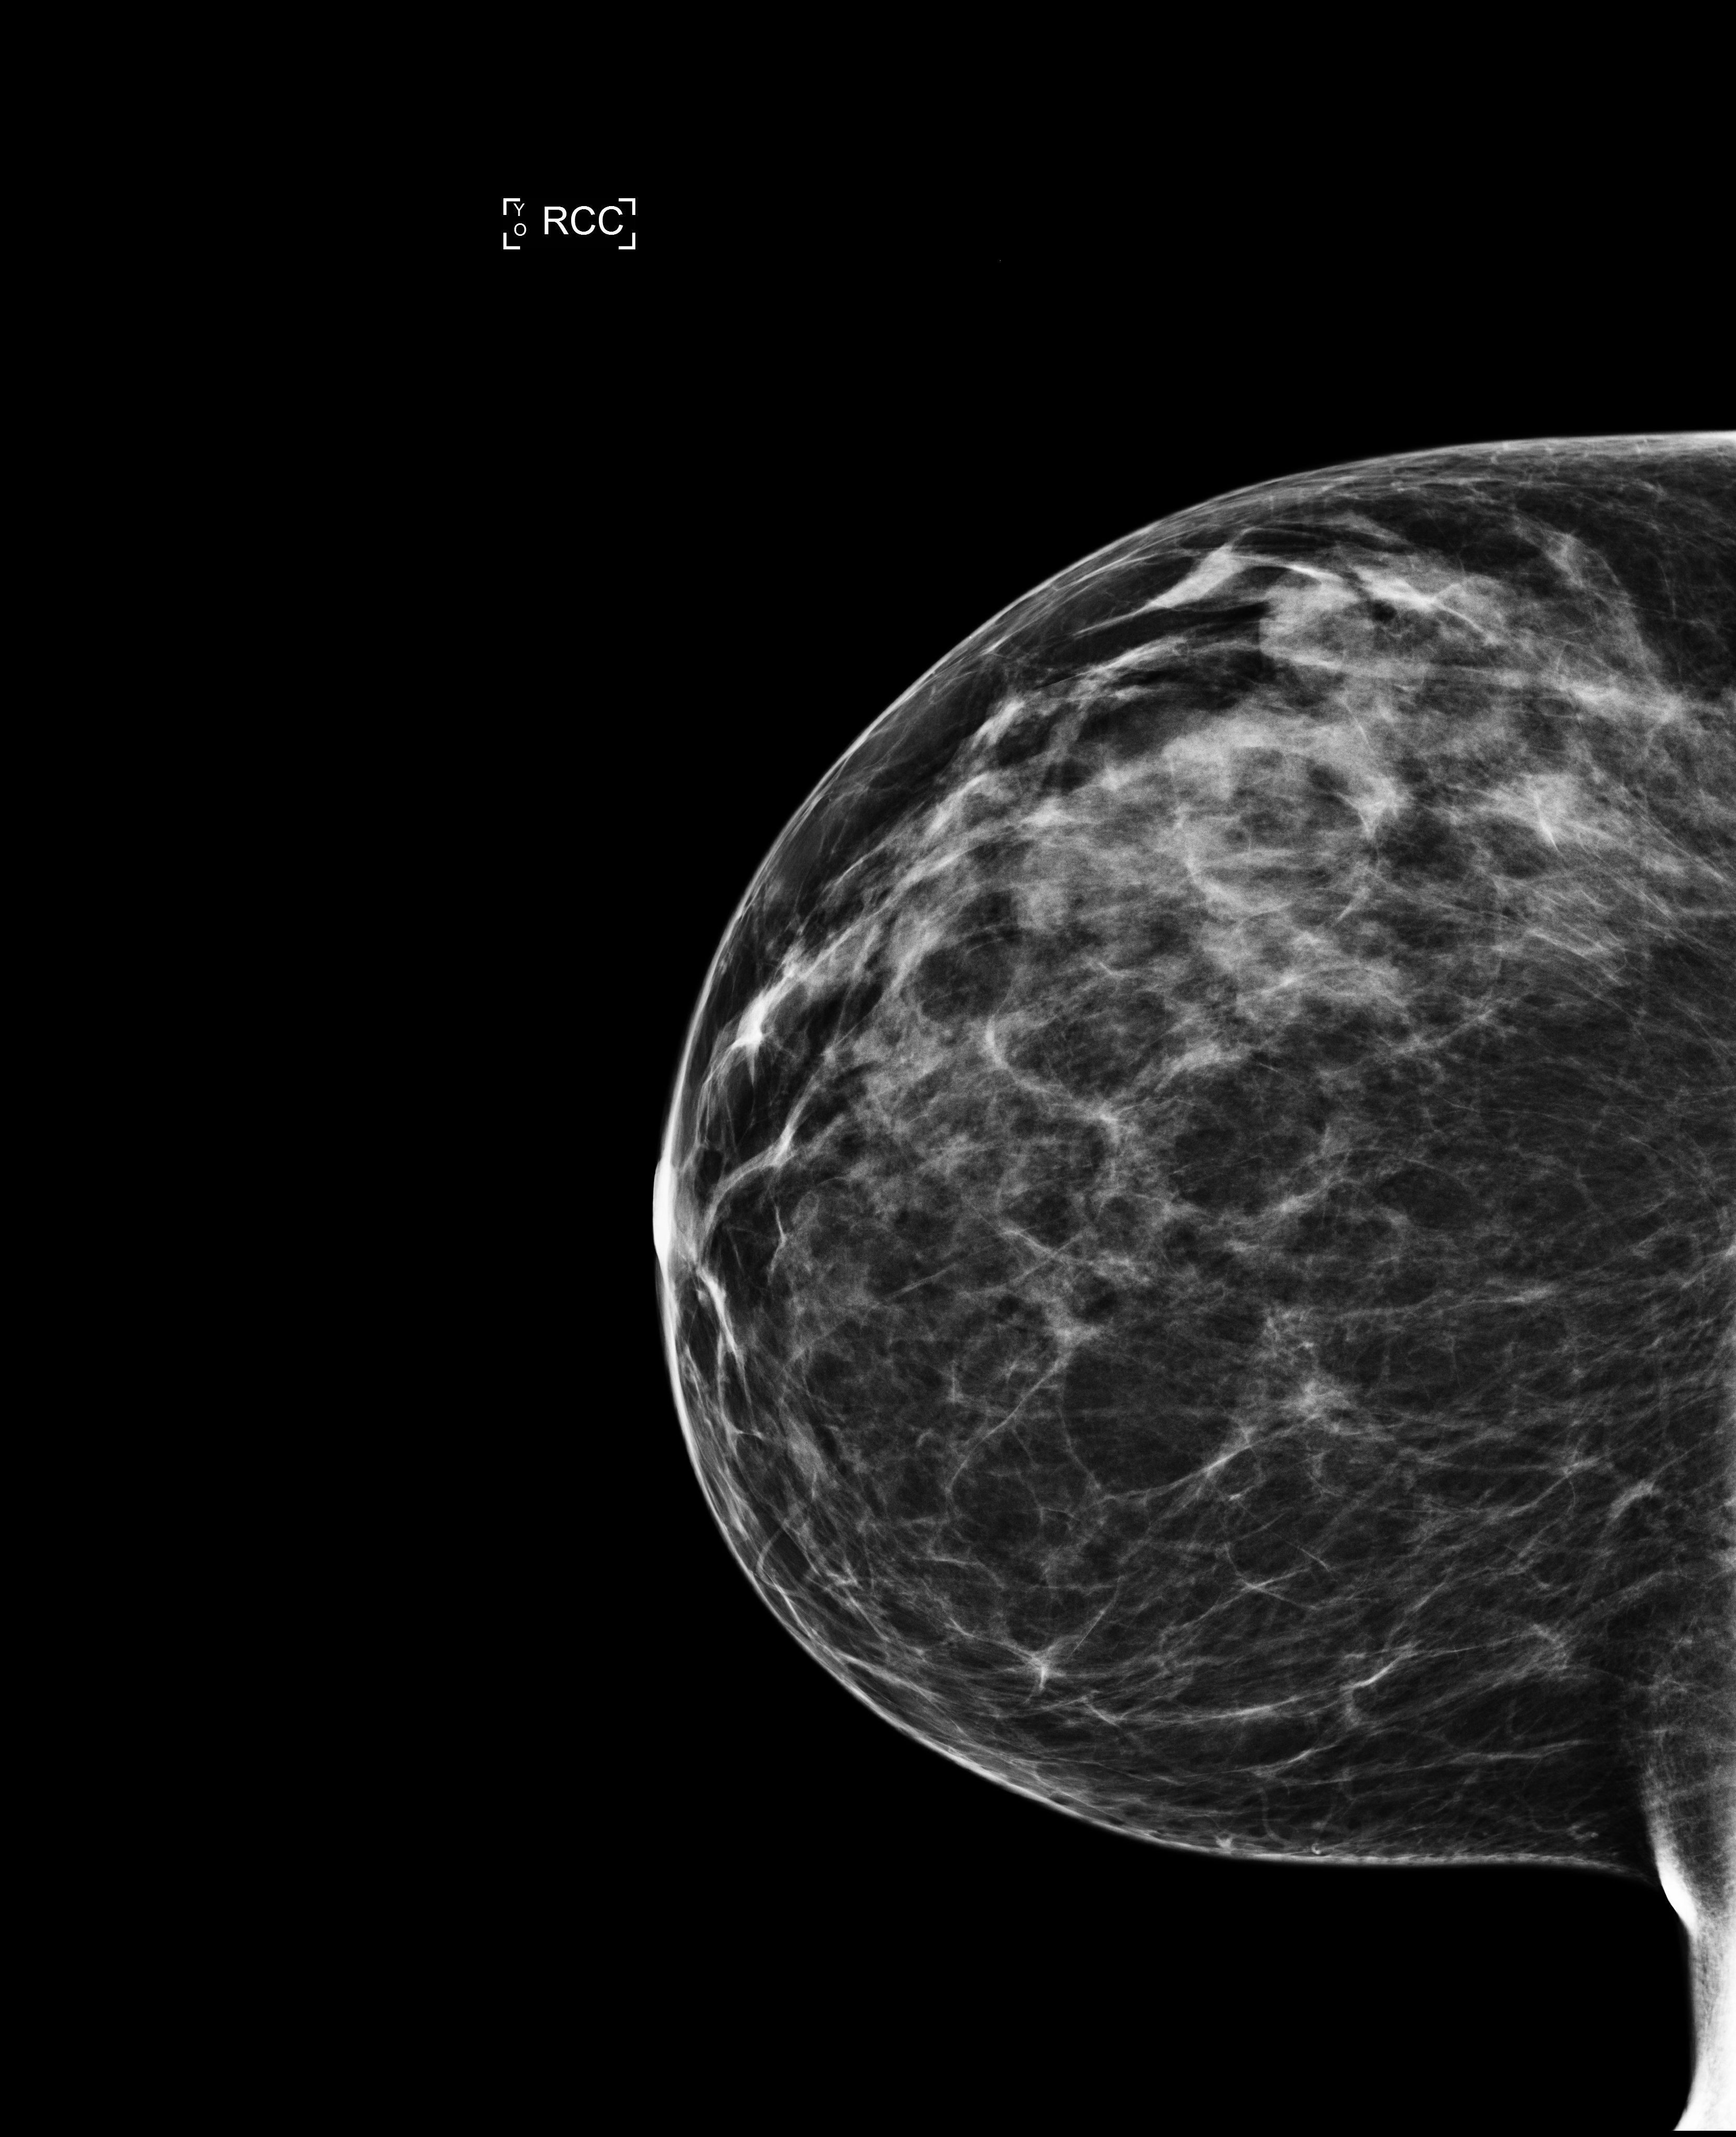
Annual screening mammography examination; system: Selenia Dimensions. Patient: female, 43 years.
Image type: full-field digital mammogram. Breast: right. Projection: CC view.